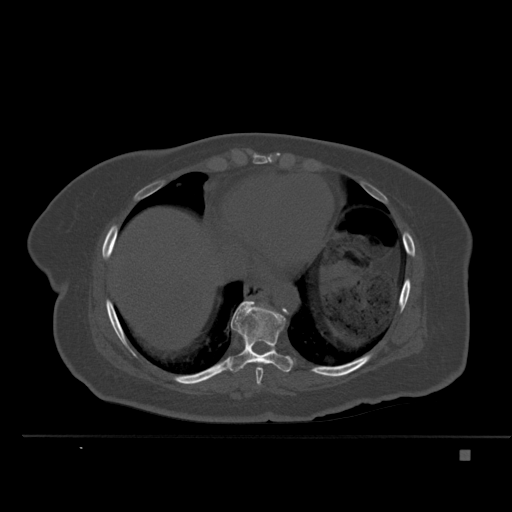
CT including the spine, one axial slice. Position 299 of 477 along the scan axis. Bone window (W 1800 / L 400 HU). 1.5 mm slice thickness. 512 × 512 image matrix, field of view 422 × 422 mm. Patient: female, 74 years. From the clinical record (not read from this slice): primary cancer: colon.
Outlined on this slice (semi-automatically segmented with operator editing):
- T8 vertebra: bounding box <256,367,263,386> (left, top, right, bottom; pixels)
- T9 vertebra: <222,300,293,373>